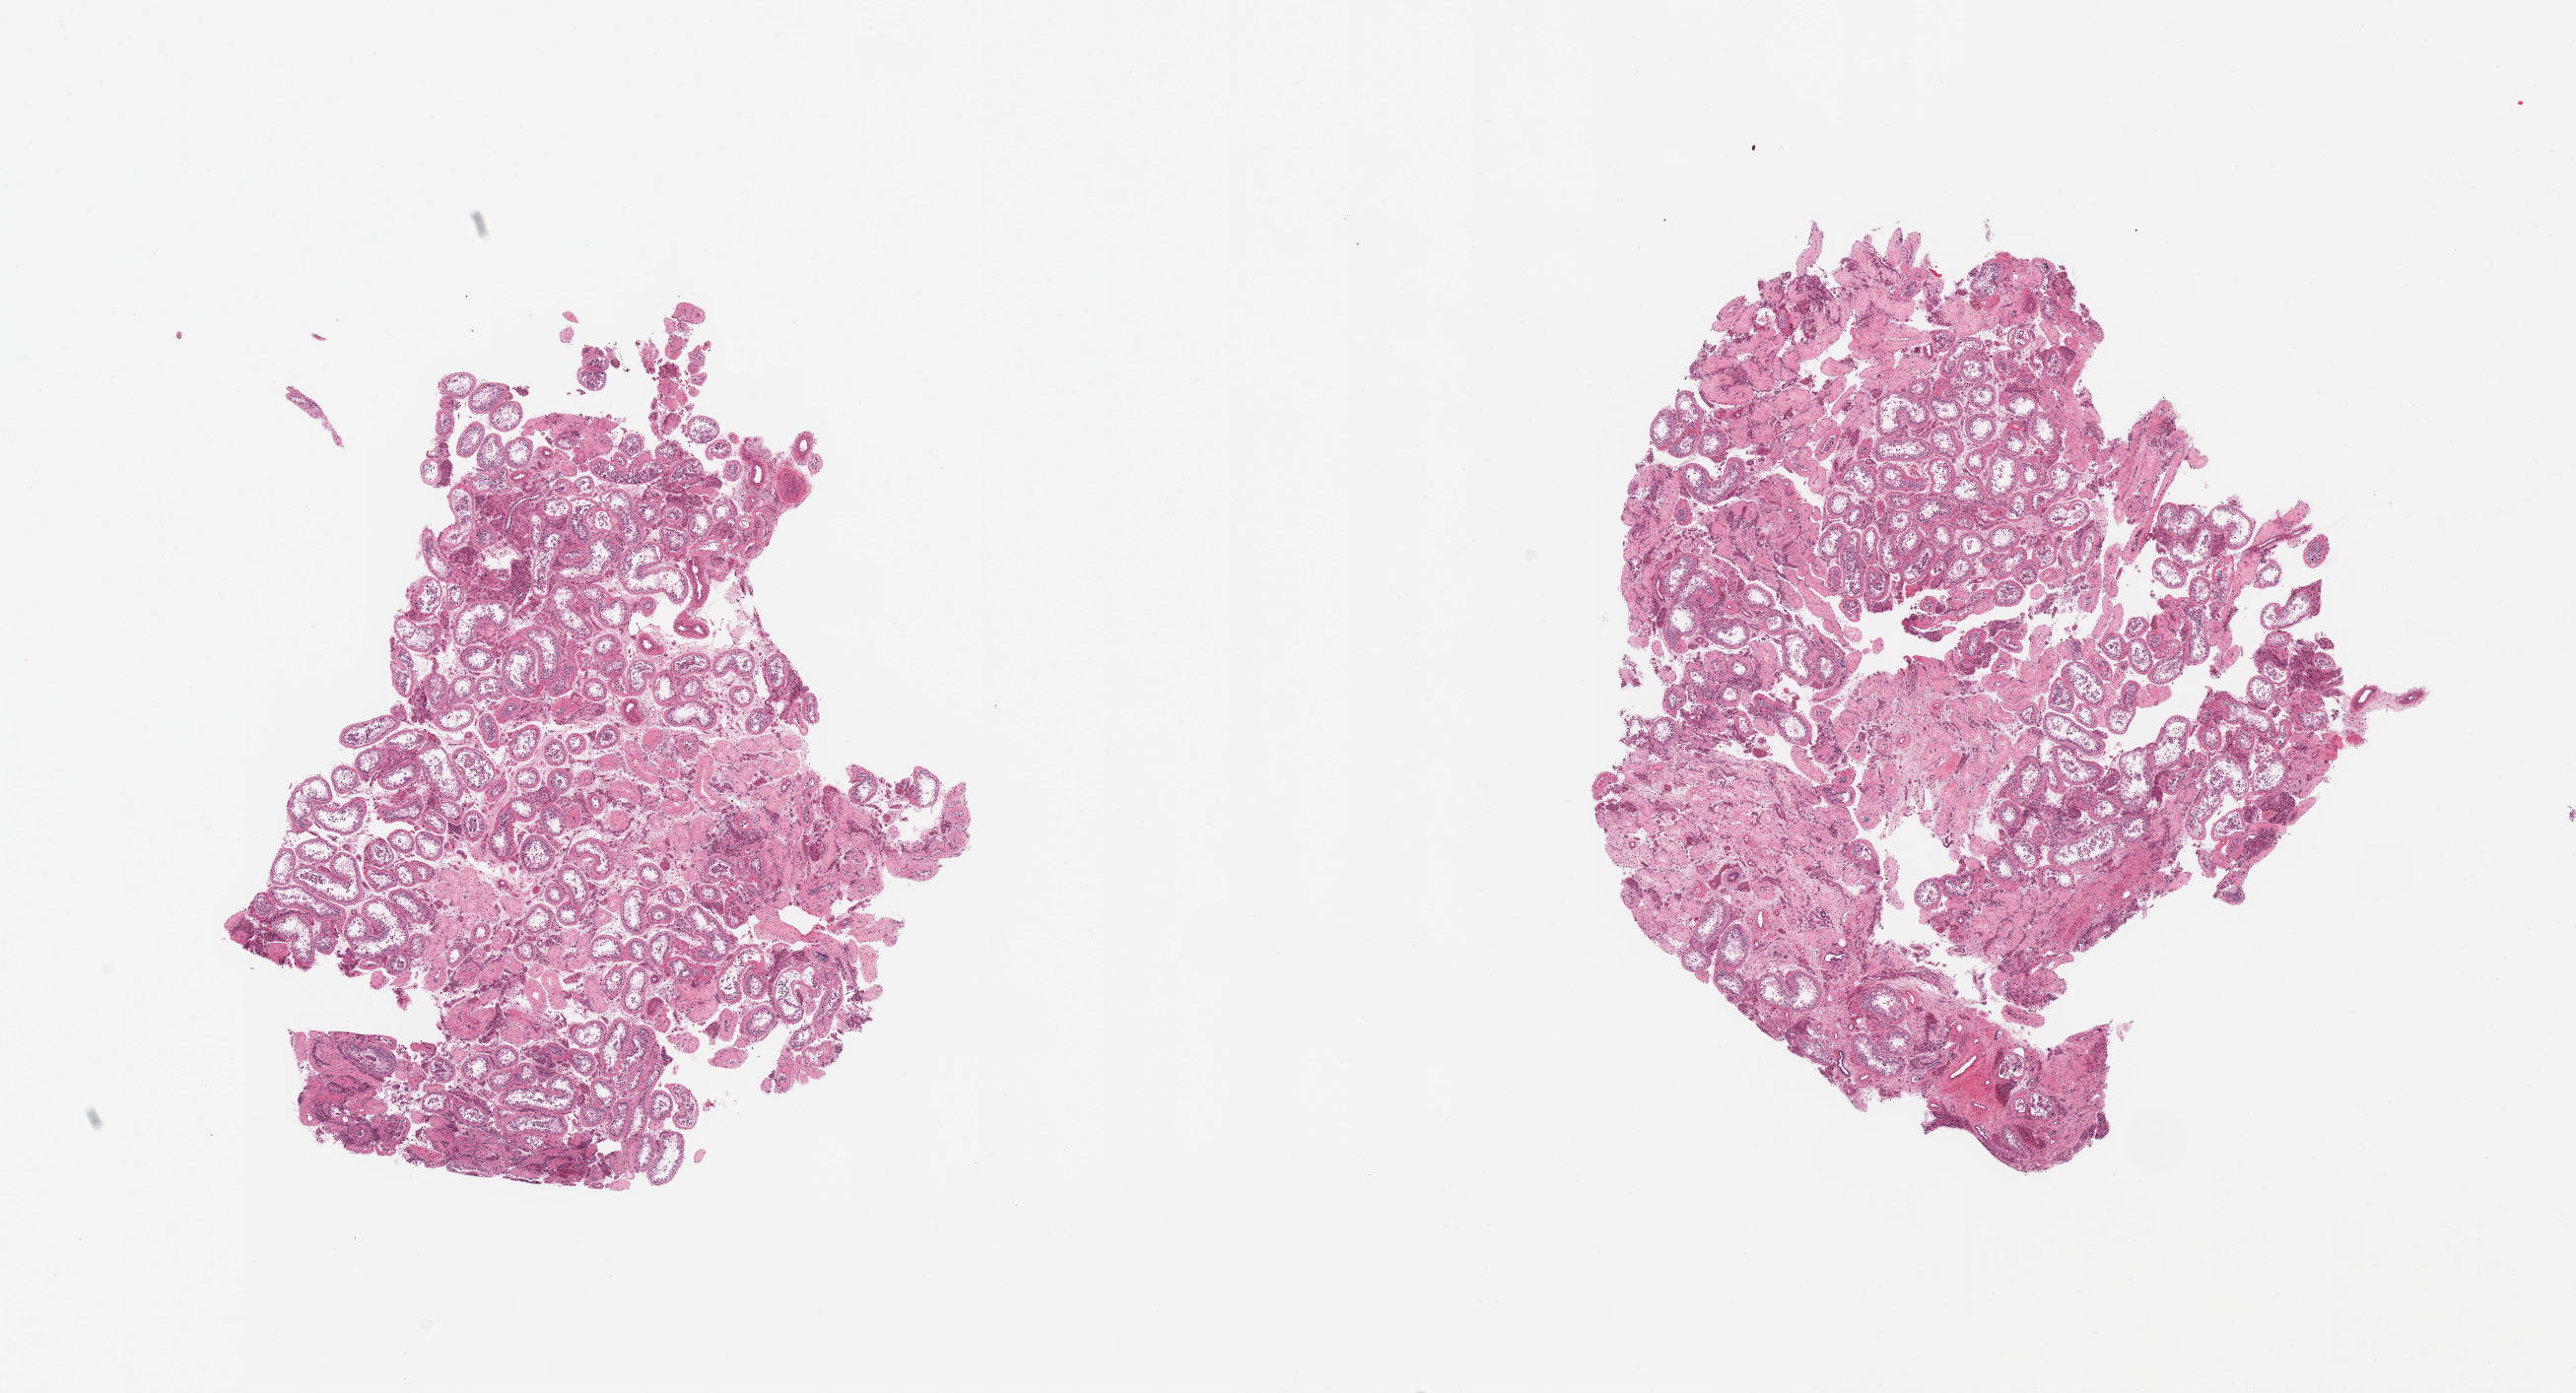
H&E whole-slide image — low-resolution overview of the scanned area, about 20.7 x 11.2 mm (acquisition: 20x scan); PAXgene-fixed paraffin-embedded (PFPE) section; target tissue: testis; donor tissue sample.
* review note (as recorded): 2 pieces; atrophy with tubular hyalinization, increased Leydig cells